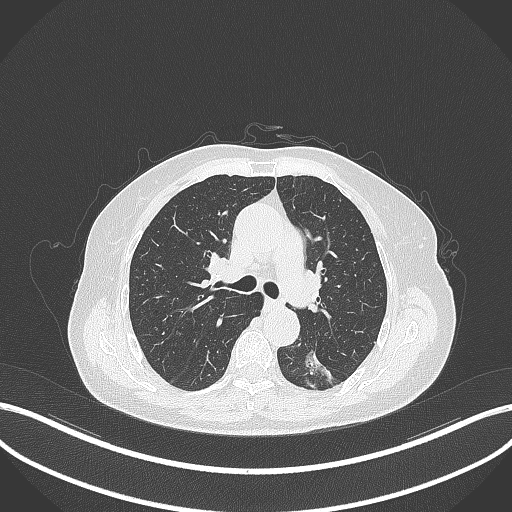
Chest CT, one axial slice; position 193 of 352 along the scan axis; reconstruction kernel B70f; lung window (W 1500 / L -600 HU); 1 mm slice thickness; 512 × 512 image matrix, field of view 400 × 400 mm. Patient: female, 70 years. From the clinical record (not read from this slice): clinical TNM (as recorded): T1c N0 M0.
Annotated regions visible in this slice (rectangle marked by the reading radiologist):
- lung tumour (recorded histology: adenocarcinoma): box from (x=301, y=346) to (x=336, y=389) px